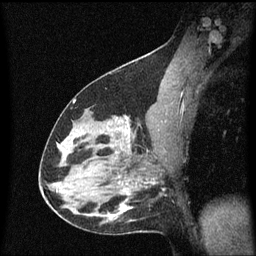
Breast MRI (dynamic contrast-enhanced), one sagittal slice; slice 34 of 60 in the series (ordered by position); dynamic contrast-enhanced series, image 2 of 3 at this slice position (ordered by acquisition); 1.5 T; TE 4.2 ms, TR 8.4 ms; 2 mm slice thickness; 256 × 256 image matrix, field of view 200 × 200 mm. Female patient, age 38 years. Case-level facts recorded for this patient, not image findings: setting: breast cancer imaged before/during neoadjuvant chemotherapy; receptor status: HR-positive, HER2-negative.
Outlined on this slice (semi-automatic segmentation, software-assisted and operator-edited):
- analysis volume of interest (the breast-tissue region the enhancement analysis was run in; not a lesion): bounding box <122,126,154,163> (left, top, right, bottom; pixels)
- tumour enhancement mask (voxels above the 70 % enhancement threshold inside the analysis volume of interest): <126,126,131,147>